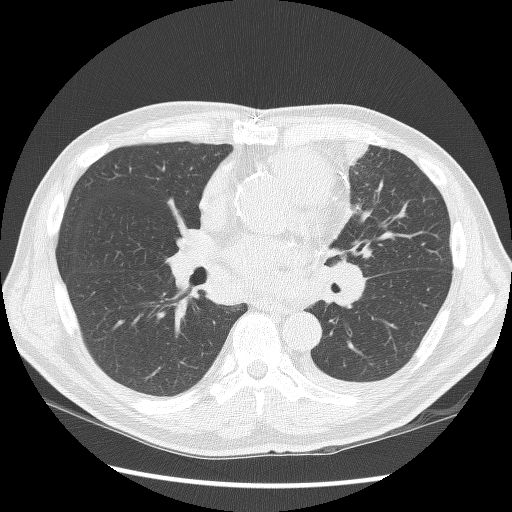
Axial slice from a low-dose chest CT screening exam; second screening round (one year after baseline); lung window (W 1500 / L -600 HU); slice 63 of 136 in the series. Male, age 64 years at enrolment. Former smoker at enrolment.
Expert reader's lesion annotation, box from (x=307, y=123) to (x=398, y=277) px. Screening reader's record for this exam: no non-calcified nodule ≥4 mm recorded. Official screen result: positive, other. Participant outcome: lung cancer diagnosed 24 days after this screen — small cell carcinoma, NOS, left upper lobe, stage IV (AJCC 6th edition), 100 mm at pathology.